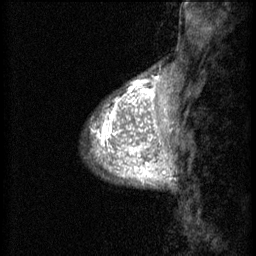
Breast MRI (dynamic contrast-enhanced), one sagittal slice; slice 11 of 60 in the series (ordered by position); 3 images stored at this slice position (order not interpretable as contrast timing); 1.5 T; TE 4.2 ms, TR 8.2 ms; 256 × 256 image matrix, field of view 180 × 180 mm. Female patient, age 38 years.
Annotated regions visible in this slice (semi-automatic segmentation, software-assisted and operator-edited):
- analysis volume of interest (the breast-tissue region the enhancement analysis was run in; not a lesion): bounding box [x1, y1, x2, y2] px = [95, 106, 157, 171]
- tumour enhancement mask (voxels above the 70 % enhancement threshold inside the analysis volume of interest): [95, 106, 157, 171]